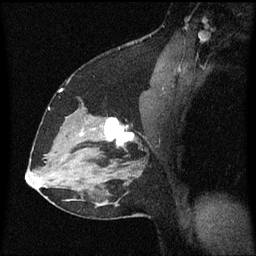
Breast MRI (dynamic contrast-enhanced), one sagittal slice. Position 40 of 60 along the scan axis. Dynamic contrast-enhanced series, image 2 of 3 at this slice position (ordered by acquisition). 1.5 T. TE 4.2 ms, TR 8.4 ms. 256 × 256 image matrix, field of view 200 × 200 mm. Female patient, age 37 years. From the clinical record (not read from this slice): setting: breast cancer imaged before/during neoadjuvant chemotherapy; receptor status: HR-positive, HER2-negative.
Structures marked on this image (semi-automatically segmented with operator editing):
- analysis volume of interest (the breast-tissue region the enhancement analysis was run in; not a lesion): bounding box (x1, y1, x2, y2) in pixels: (94, 116, 141, 157)
- tumour enhancement mask (voxels above the 70 % enhancement threshold inside the analysis volume of interest): (105, 118, 135, 147)